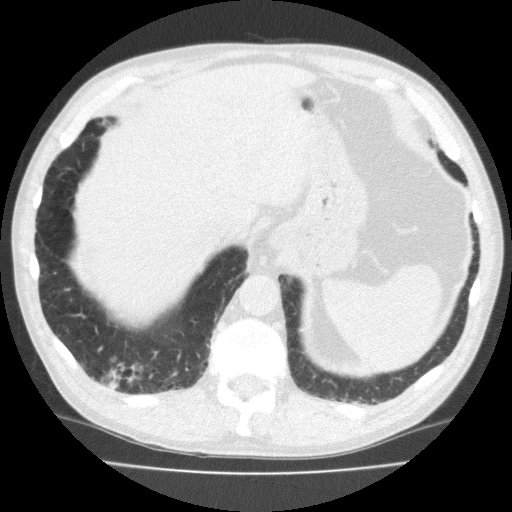
Chest CT (low-dose screening protocol), one axial image, second screening round (one year after baseline), lung window (W 1500 / L -600 HU), 2 mm slice thickness, standard (soft-tissue) reconstruction kernel (FC10), slice 150 of 195 in the series. Male participant, aged 70 years at enrolment.
- Expert-annotated lung lesion, bounding box (x1, y1, x2, y2) in pixels: (85, 349, 160, 400).
- Reader record for this screening exam (exam-level; its link to the box is not recorded): non-calcified nodule or mass ≥4 mm, right lower lobe, 18 × 13 mm, spiculated (stellate) margins, soft tissue attenuation, pre-existing on the prior screen: no.
- Later outcome: lung cancer diagnosed 64 days after this screen — squamous cell carcinoma, NOS, right lower lobe, moderately differentiated (G2), stage IA (AJCC 6th edition), 20 mm at pathology.